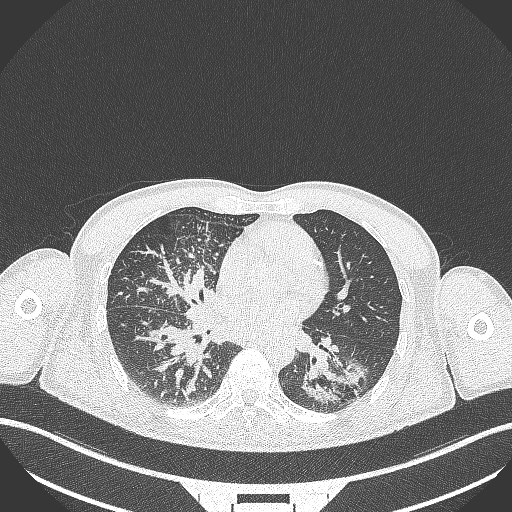
Chest CT, one axial slice. Slice 148 of 348 in the series (ordered by position). Lung window (W 1500 / L -600 HU). 1 mm slice thickness. 512 × 512 image matrix, field of view 400 × 400 mm. Male patient, age 49 years. Case-level facts recorded for this patient, not image findings: clinical TNM (as recorded): T2b N1 M0.
Structures marked on this image (bounding box drawn by a radiologist):
- lung tumour (recorded histology: adenocarcinoma): box from (x=289, y=349) to (x=371, y=415) px